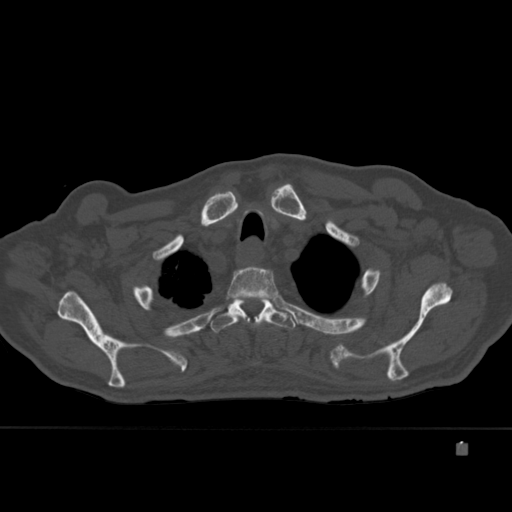
CT including the spine, one axial slice; slice 340 of 451 in the series (ordered by position); bone window (W 1800 / L 400 HU); 512 × 512 image matrix, field of view 378 × 378 mm. Patient: male, 75 years. From the clinical record (not read from this slice): primary cancer: prostate.
Outlined on this slice (semi-automatically segmented with operator editing):
- T2 vertebra: bounding box (x1, y1, x2, y2) in pixels: (226, 266, 278, 317)
- T3 vertebra: (210, 297, 296, 333)